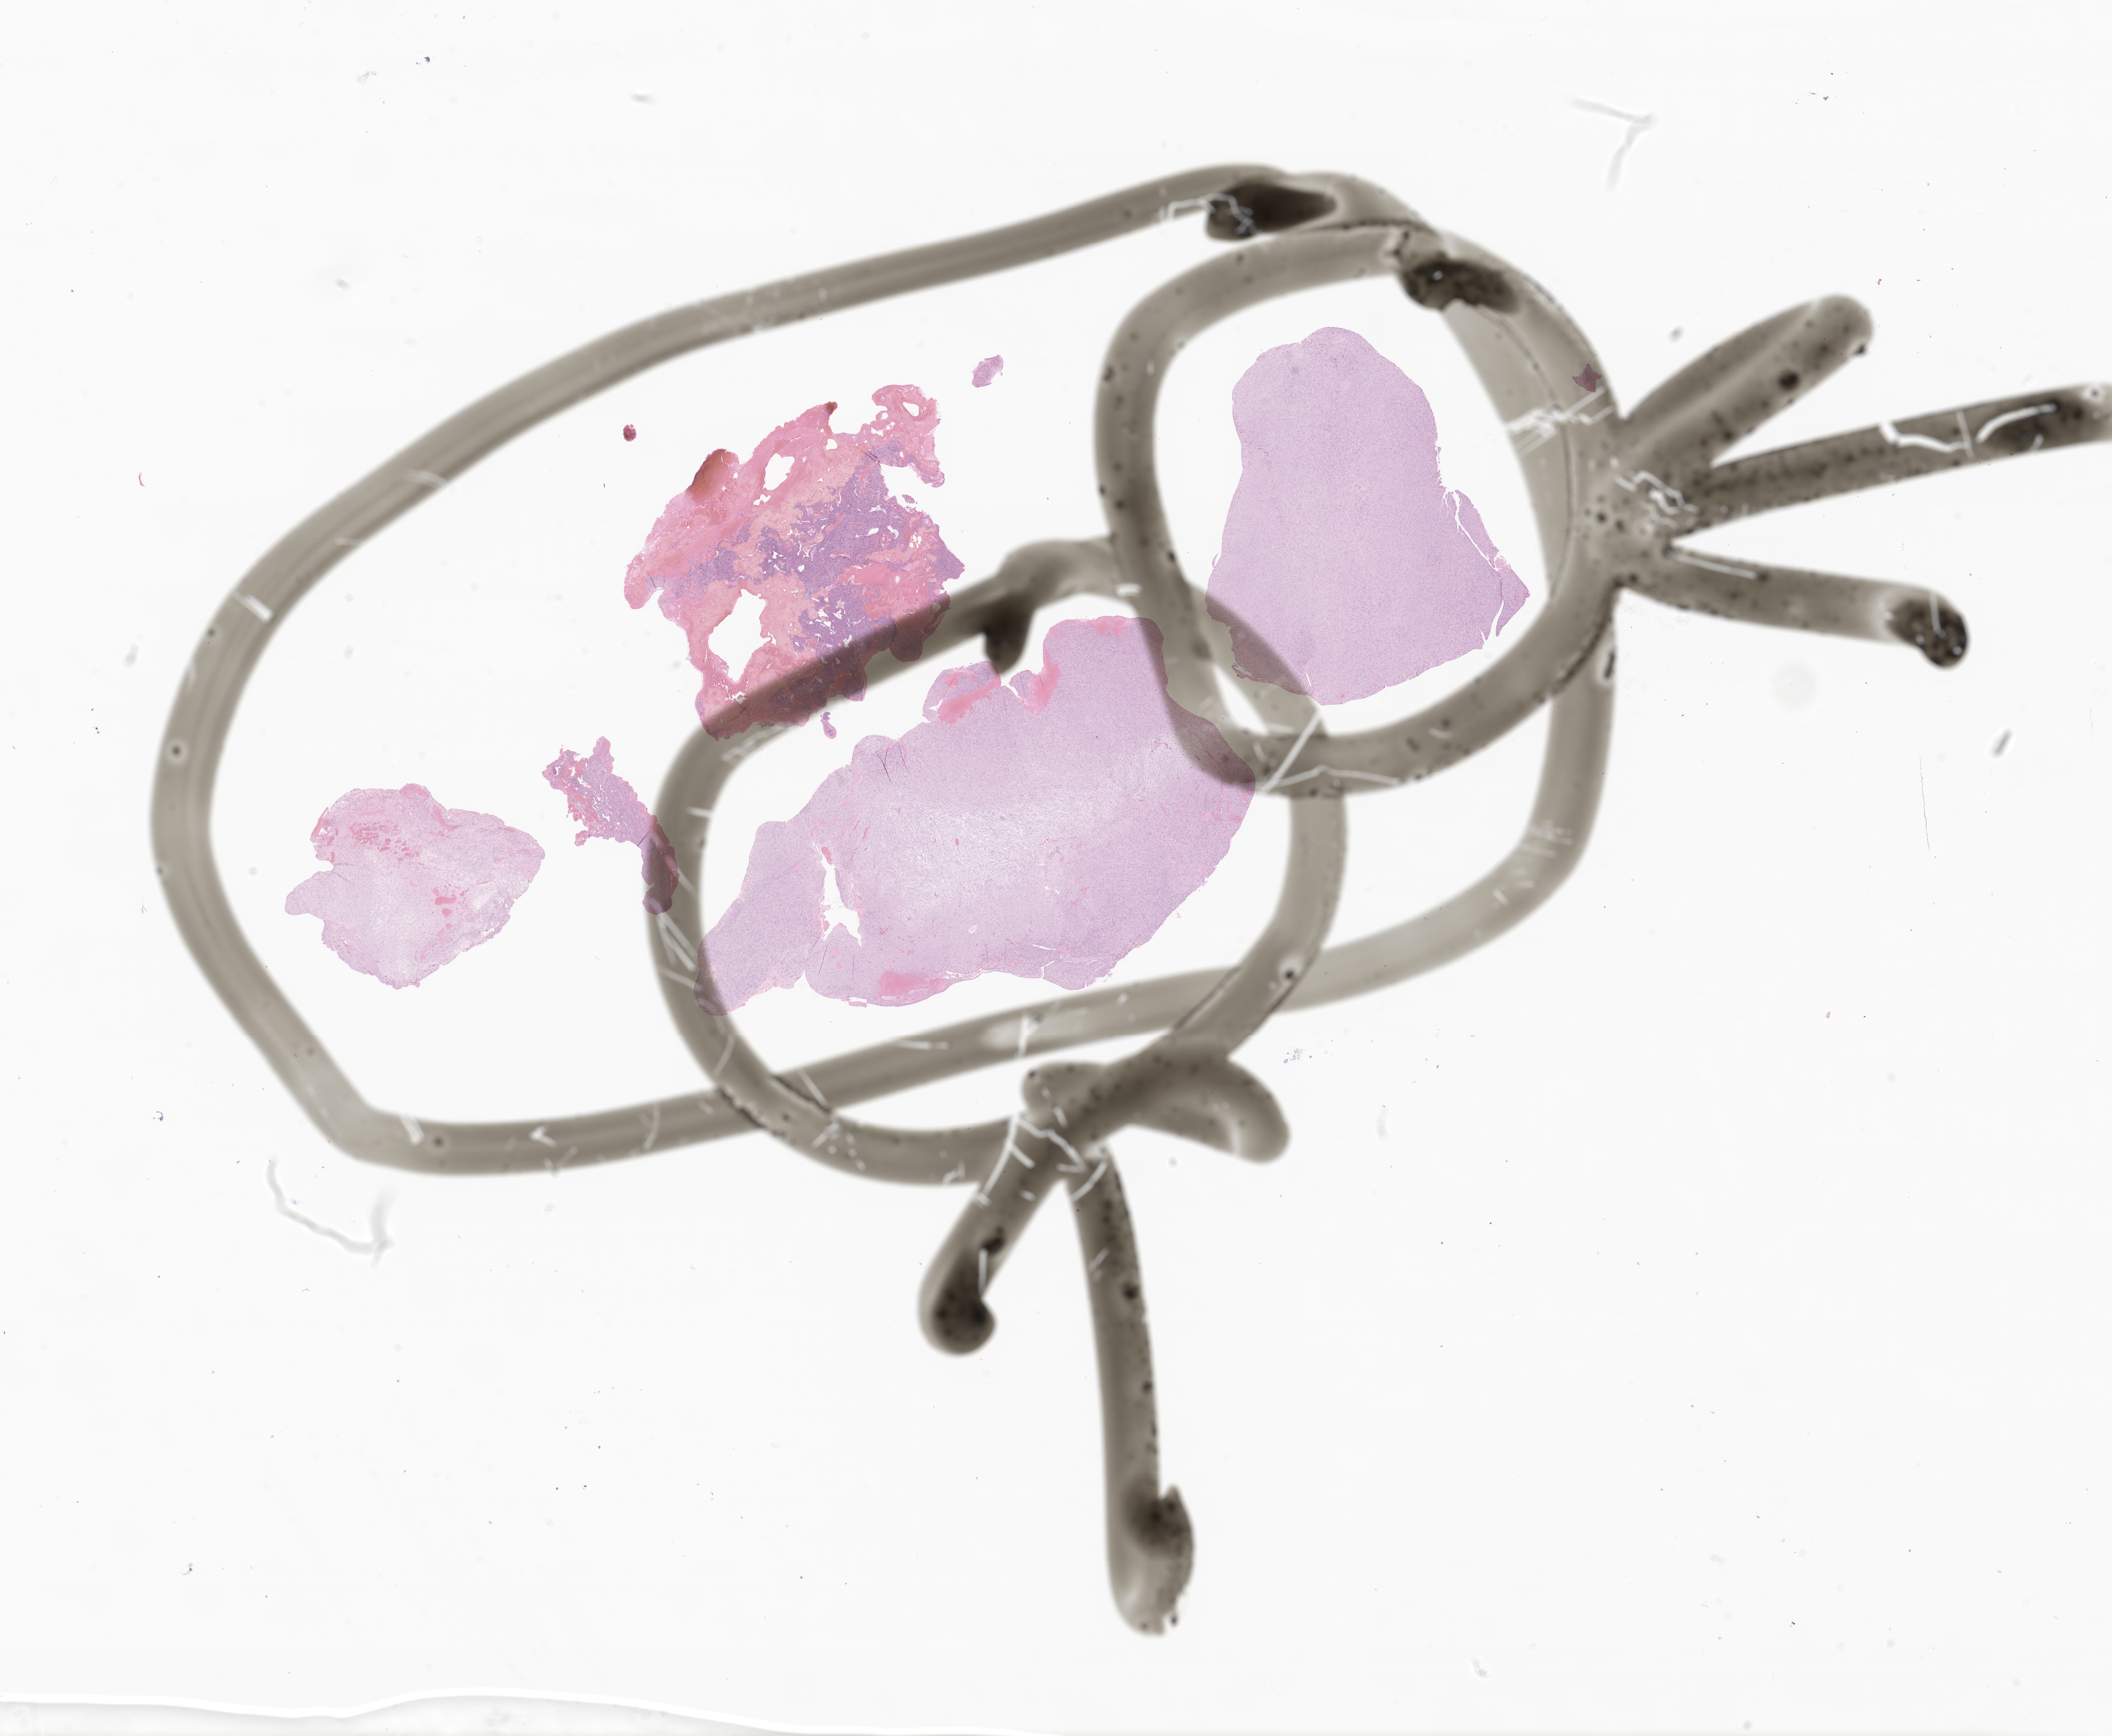
Digitized H&E-stained section of tumor tissue from the brain, low-resolution overview of the scanned area, about 25.6 x 21.0 mm. Formalin-fixed paraffin-embedded section. Female patient, age 199 months (16 years 7 months).
Diagnosis: Neoplasm, benign.